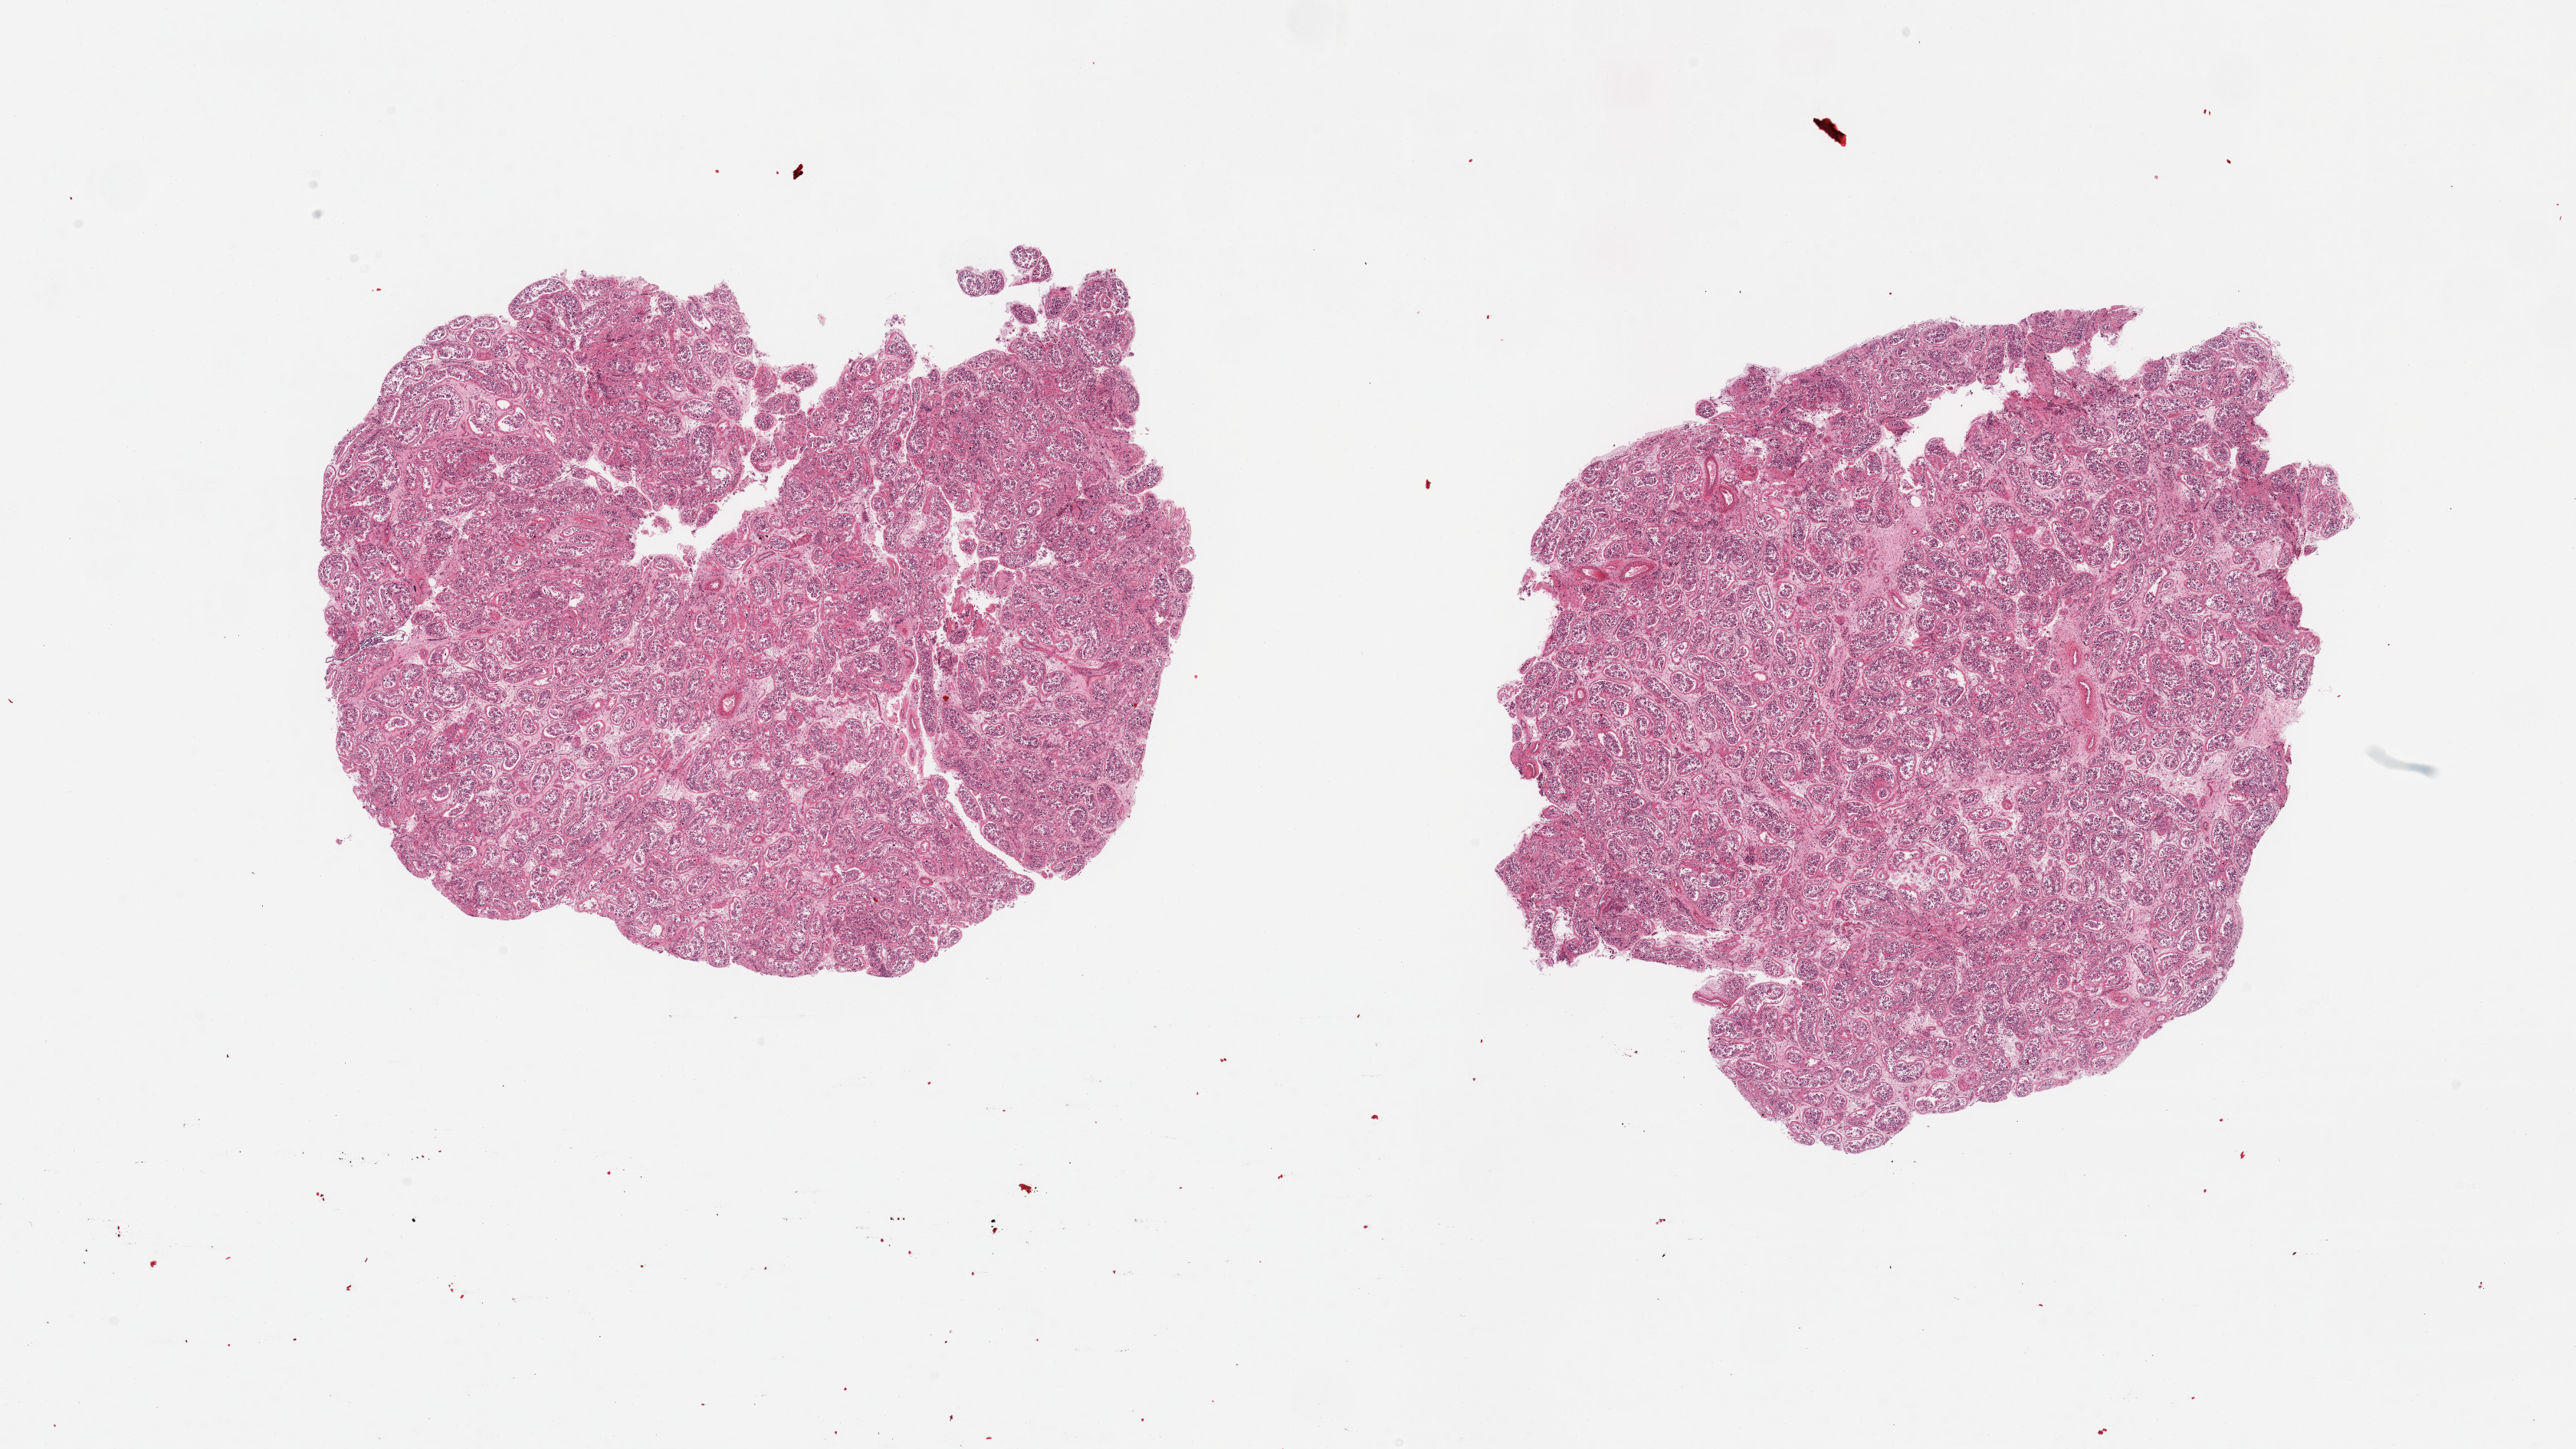
Whole-slide image, haematoxylin and eosin stain, brightfield, low-resolution overview of the scanned area, about 26.6 x 15.0 mm (slide scanned at 20x); PAXgene-fixed paraffin-embedded (PFPE) section; target tissue: testis; tissue donor sample. Male donor.
- reviewer comment on this tissue sample: 2 pieces; spermatogenesis present